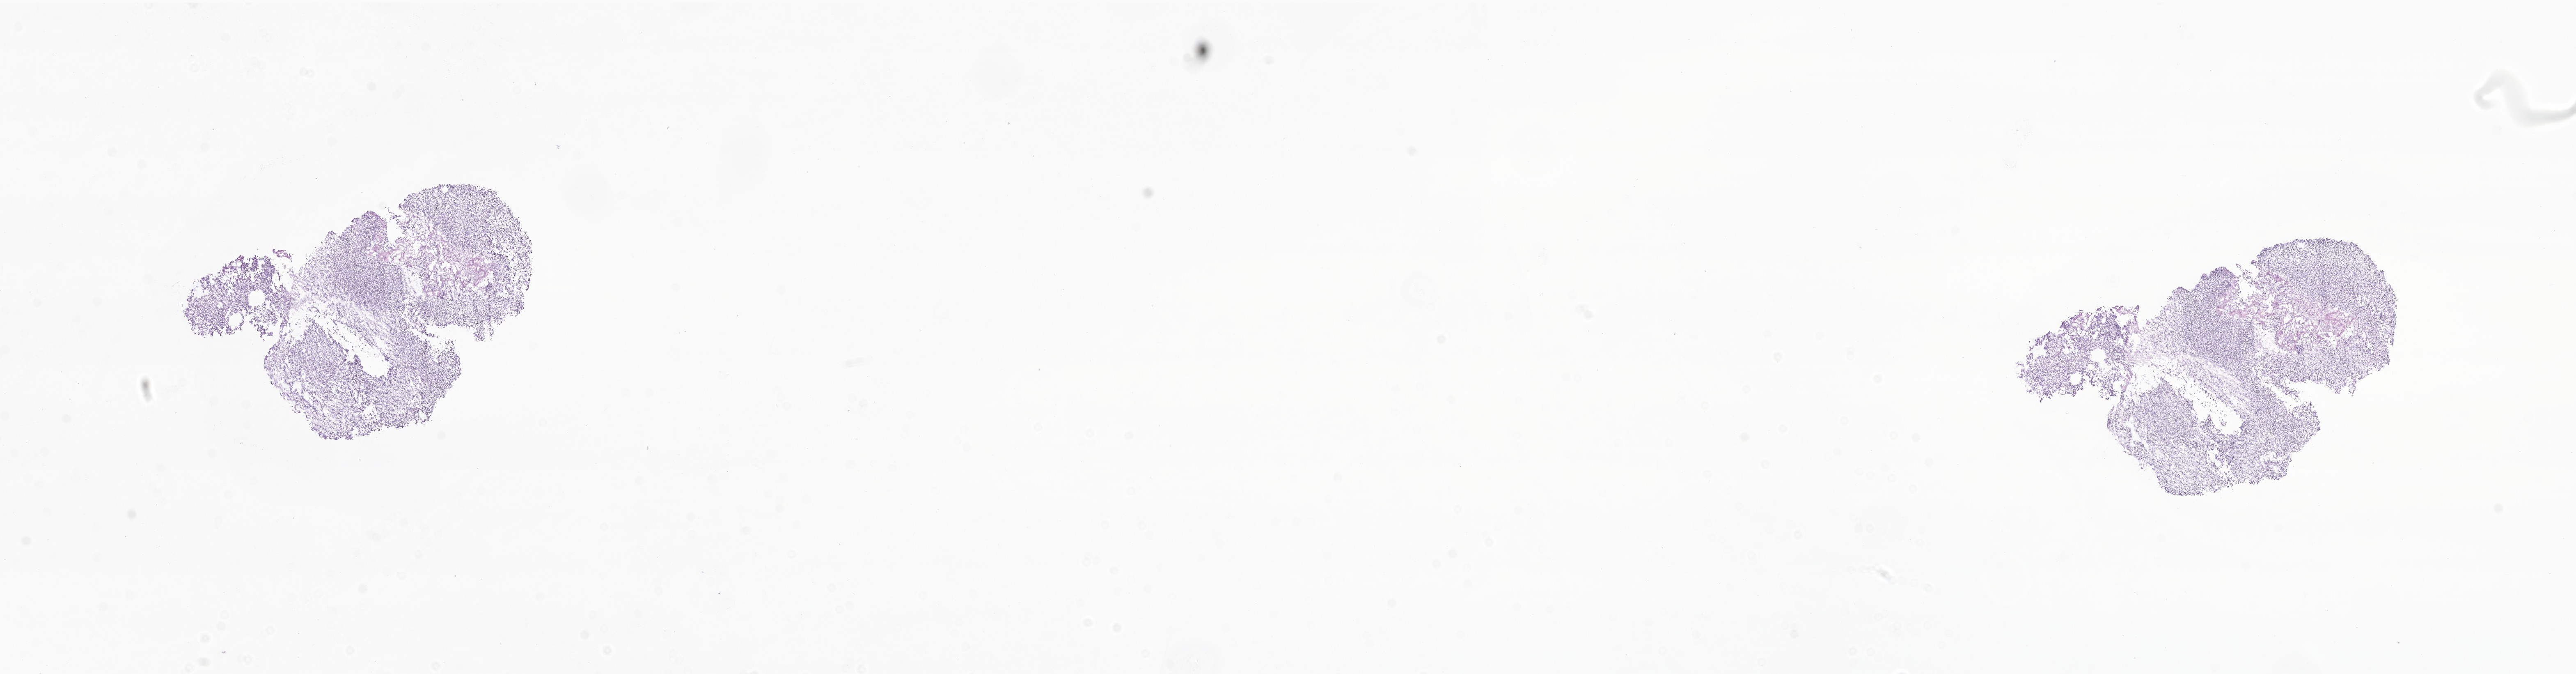
H&E whole-slide image of tumor tissue from the brain, a low-resolution overview of the entire scanned area, about 26.5 x 6.9 mm, frozen section. Male patient, age 51 months.
Recorded diagnosis: Medulloblastoma, NOS.